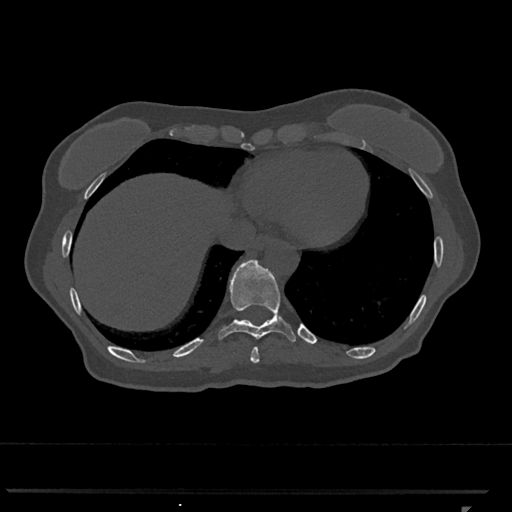
CT including the spine, one axial slice; position 571 of 793 along the scan axis; reconstruction kernel Br40s/3; 120 kVp; bone window (W 1800 / L 400 HU); 512 × 512 image matrix. Patient: female, 62 years. From the clinical record (not read from this slice): primary cancer: renal.
Annotated regions visible in this slice (semi-automatically segmented with operator editing):
- T10 vertebra: bounding box (x1, y1, x2, y2) in pixels: (218, 260, 296, 342)
- T9 vertebra: (250, 347, 260, 363)